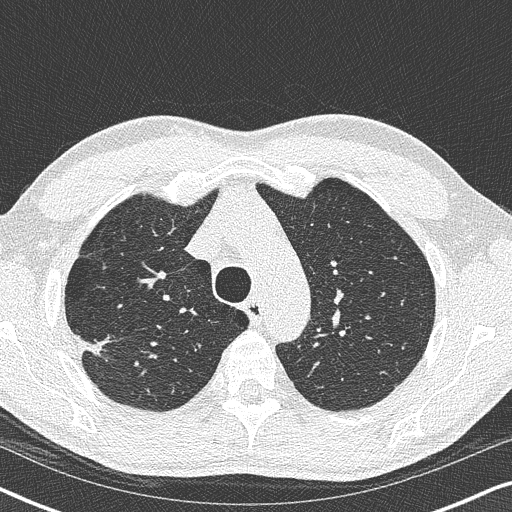
Low-dose screening chest CT, one axial slice. Position 282 of 356 along the scan axis. 120 kVp. Lung window (W 1500 / L -600 HU). 512 × 512 image matrix, field of view 330 × 330 mm.
Annotated regions visible in this slice (expert manual segmentation):
- lesion 1 (tumor, upper lobe of right lung): bounding box <81,338,102,354> (left, top, right, bottom; pixels)